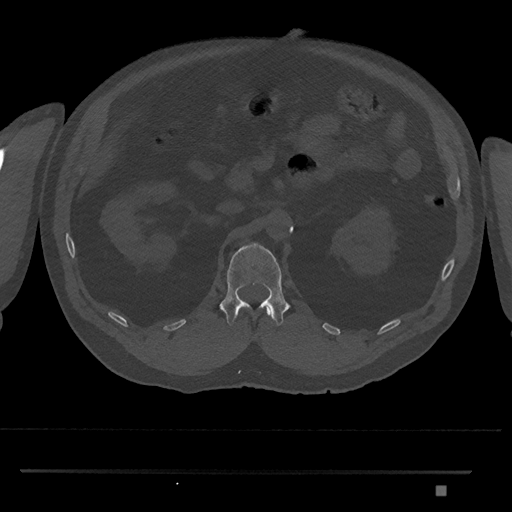
CT including the spine, one axial slice; position 834 of 1134 along the scan axis; 120 kVp; bone window (W 1800 / L 400 HU); 0.5 mm slice thickness; 512 × 512 image matrix, field of view 429 × 429 mm. Male patient, age 65 years. From the clinical record (not read from this slice): primary cancer: prostate.
Outlined on this slice (semi-automatically segmented with operator editing):
- L1 vertebra: bounding box <219,243,290,326> (left, top, right, bottom; pixels)
- T12 vertebra: <266,308,272,317>